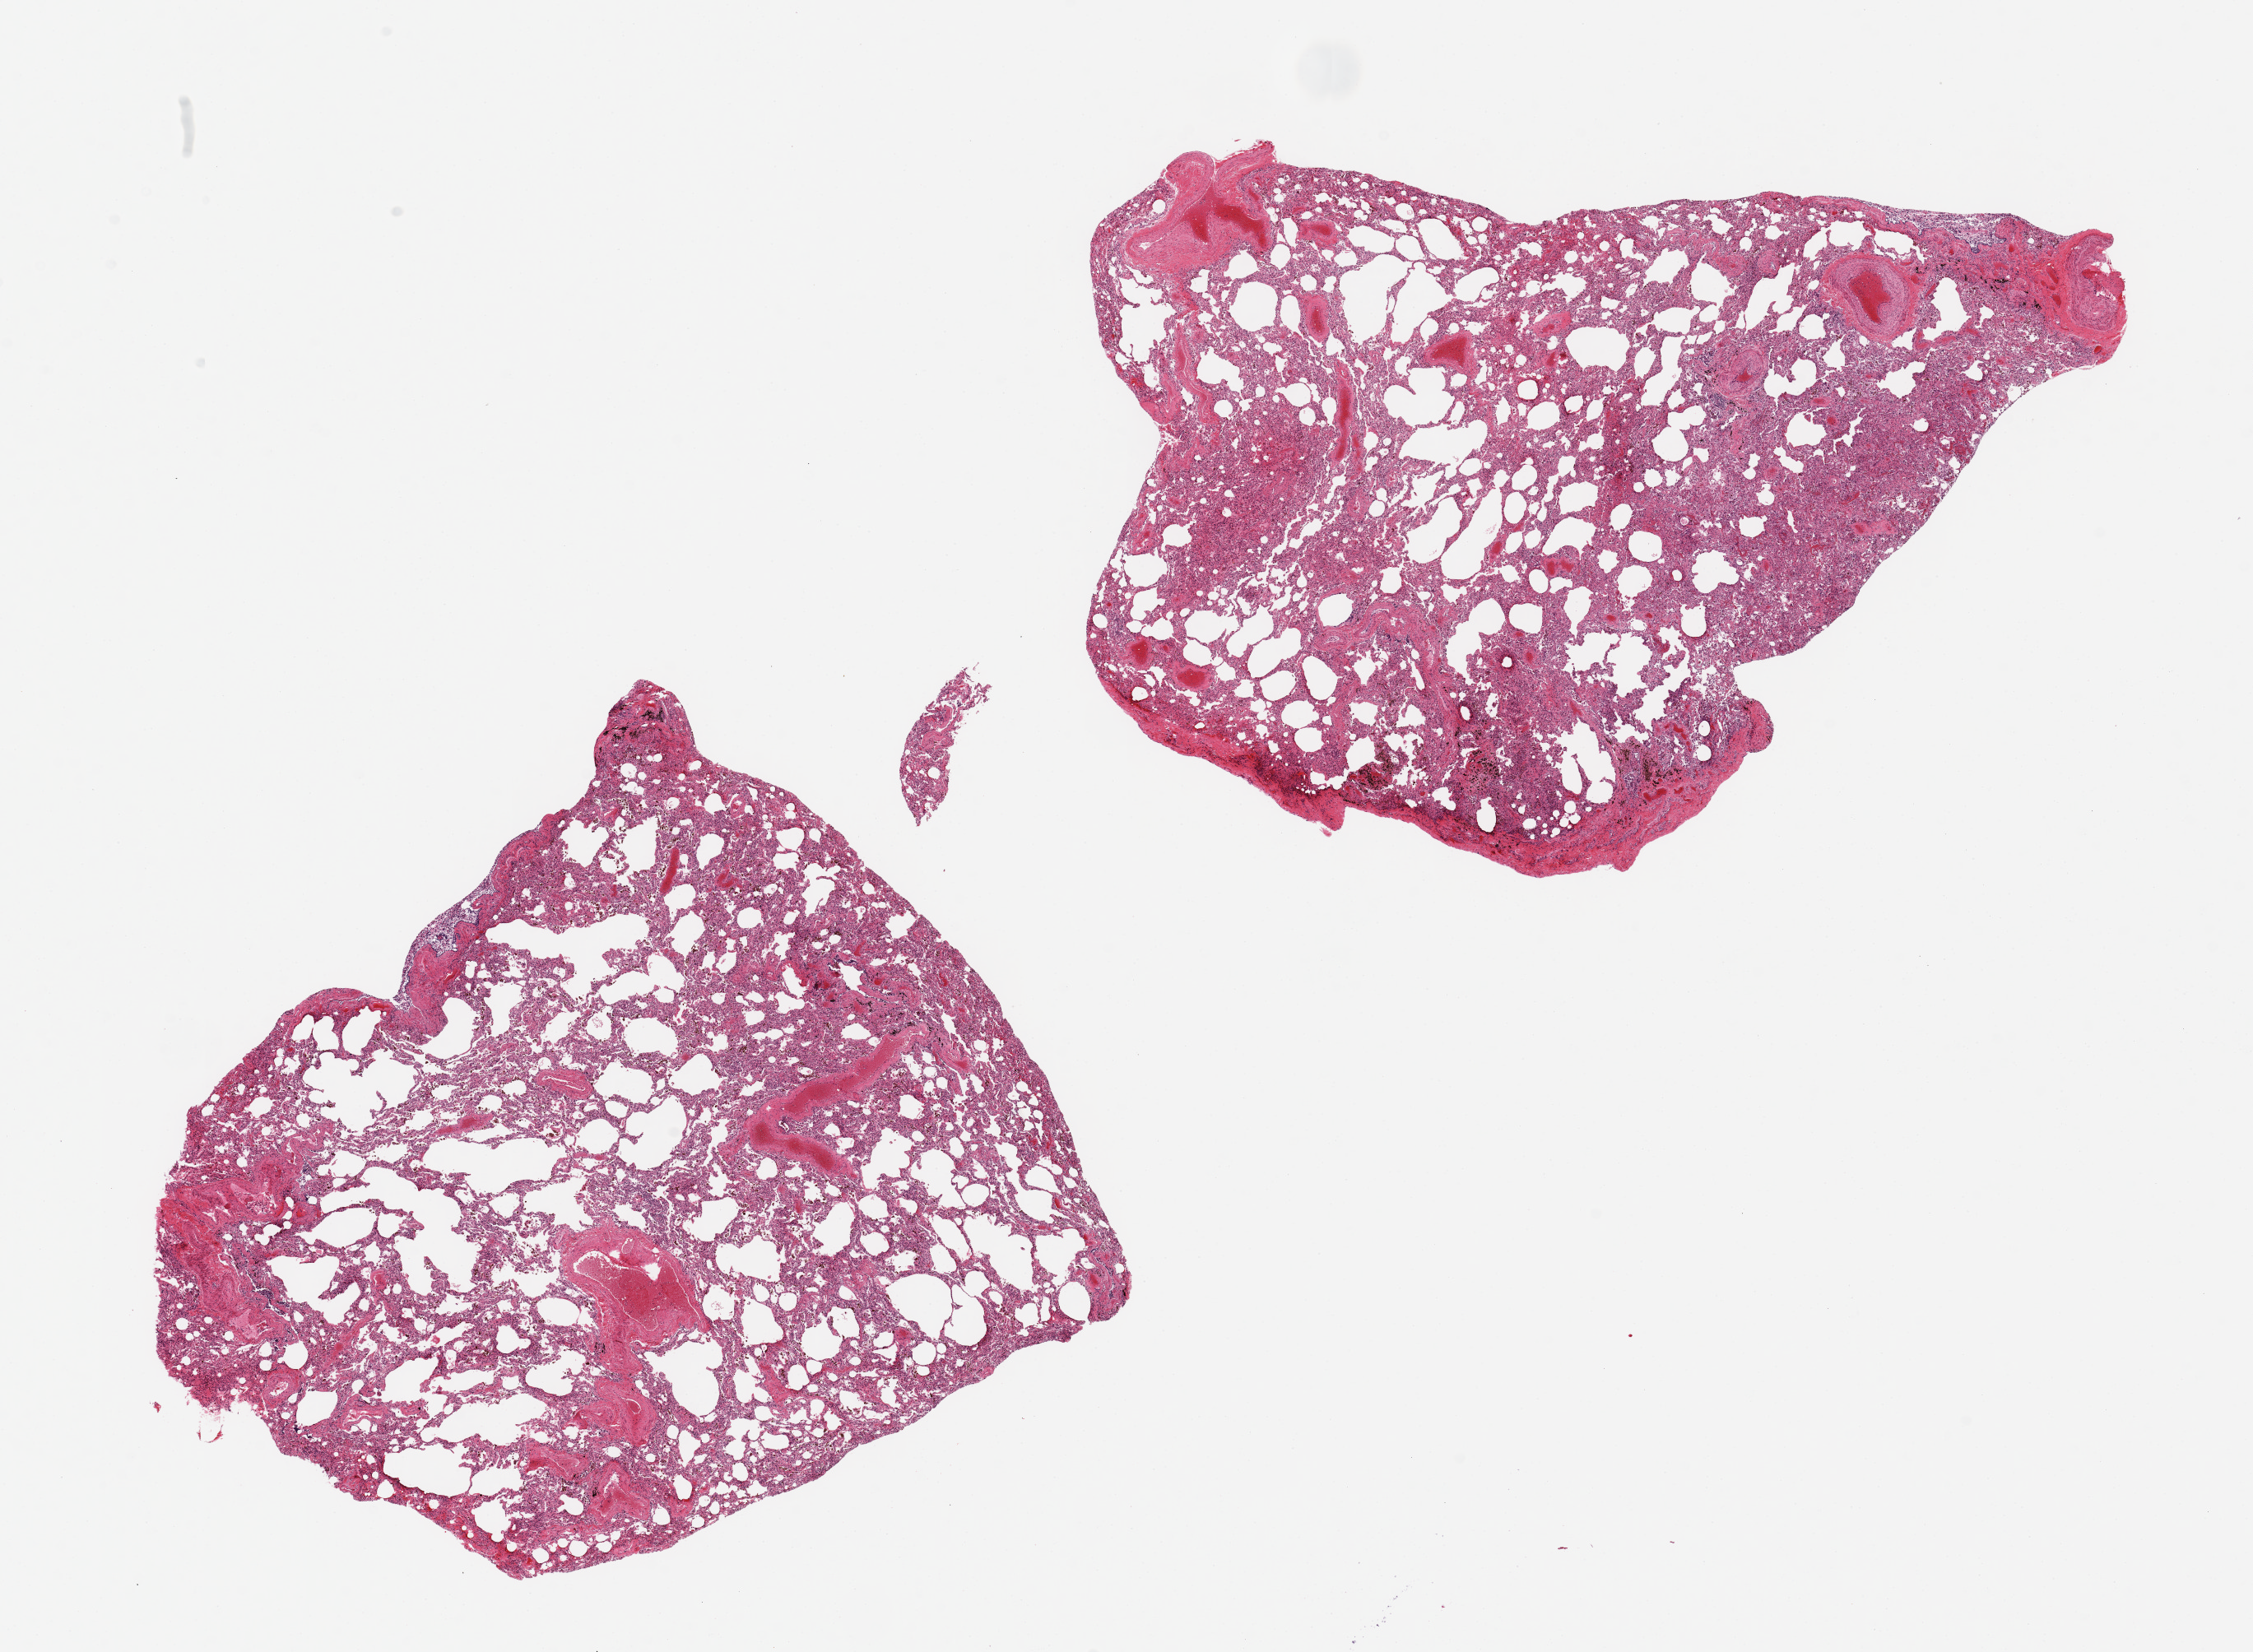
Hematoxylin and eosin (H&E) whole-slide image — shown as a low-resolution overview of the whole scanned area (about 21.7 x 15.9 mm). PAXgene-fixed, paraffin-embedded tissue. Section of lung (target tissue). Tissue donor sample. Male donor.
- review note (as recorded): 2 pieces 8x8 & 8x7 mm; numerous 'heart failure' cells, moderate alveolar dilatation; patchy alveolar hemorrhage